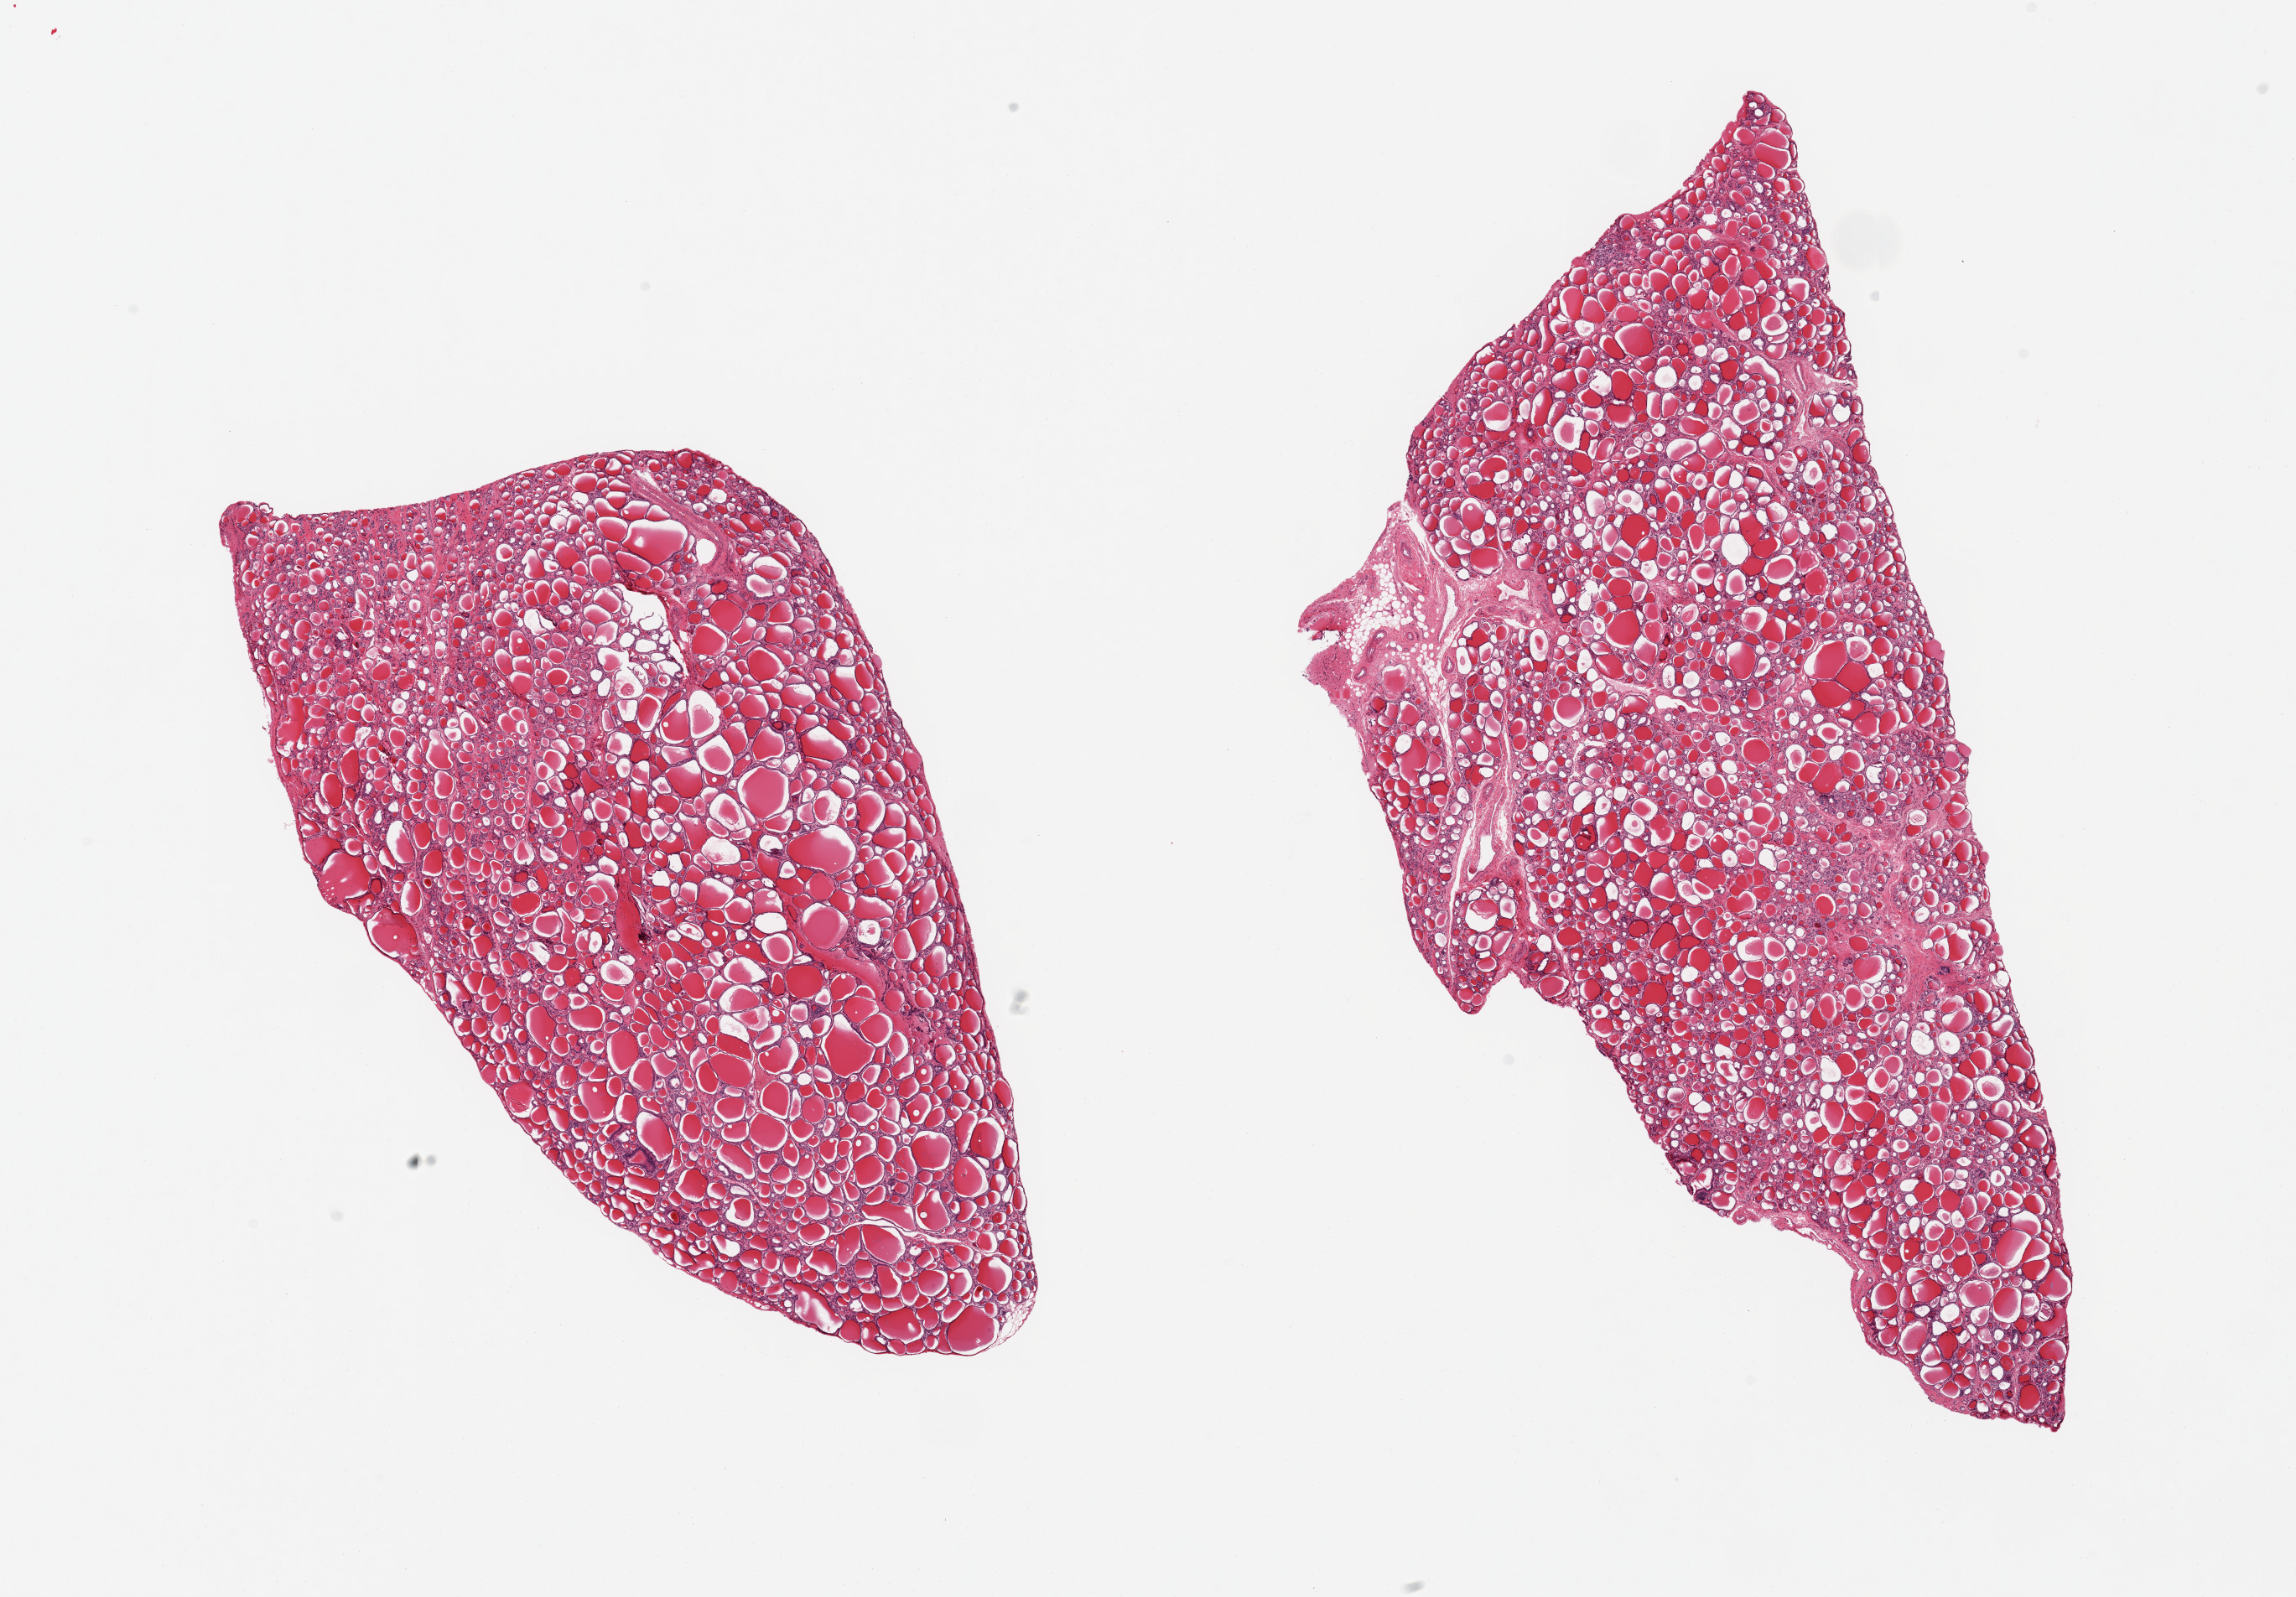
Digitized haematoxylin and eosin-stained section — whole scanned area (about 21.7 x 15.1 mm, acquisition: 20x scan) shown as a low-resolution overview; PAXgene-fixed paraffin-embedded (PFPE) section; section of thyroid (target tissue); donor tissue sample. Donor sex: female.
* pathologist's review note for this sample: 2 pieces